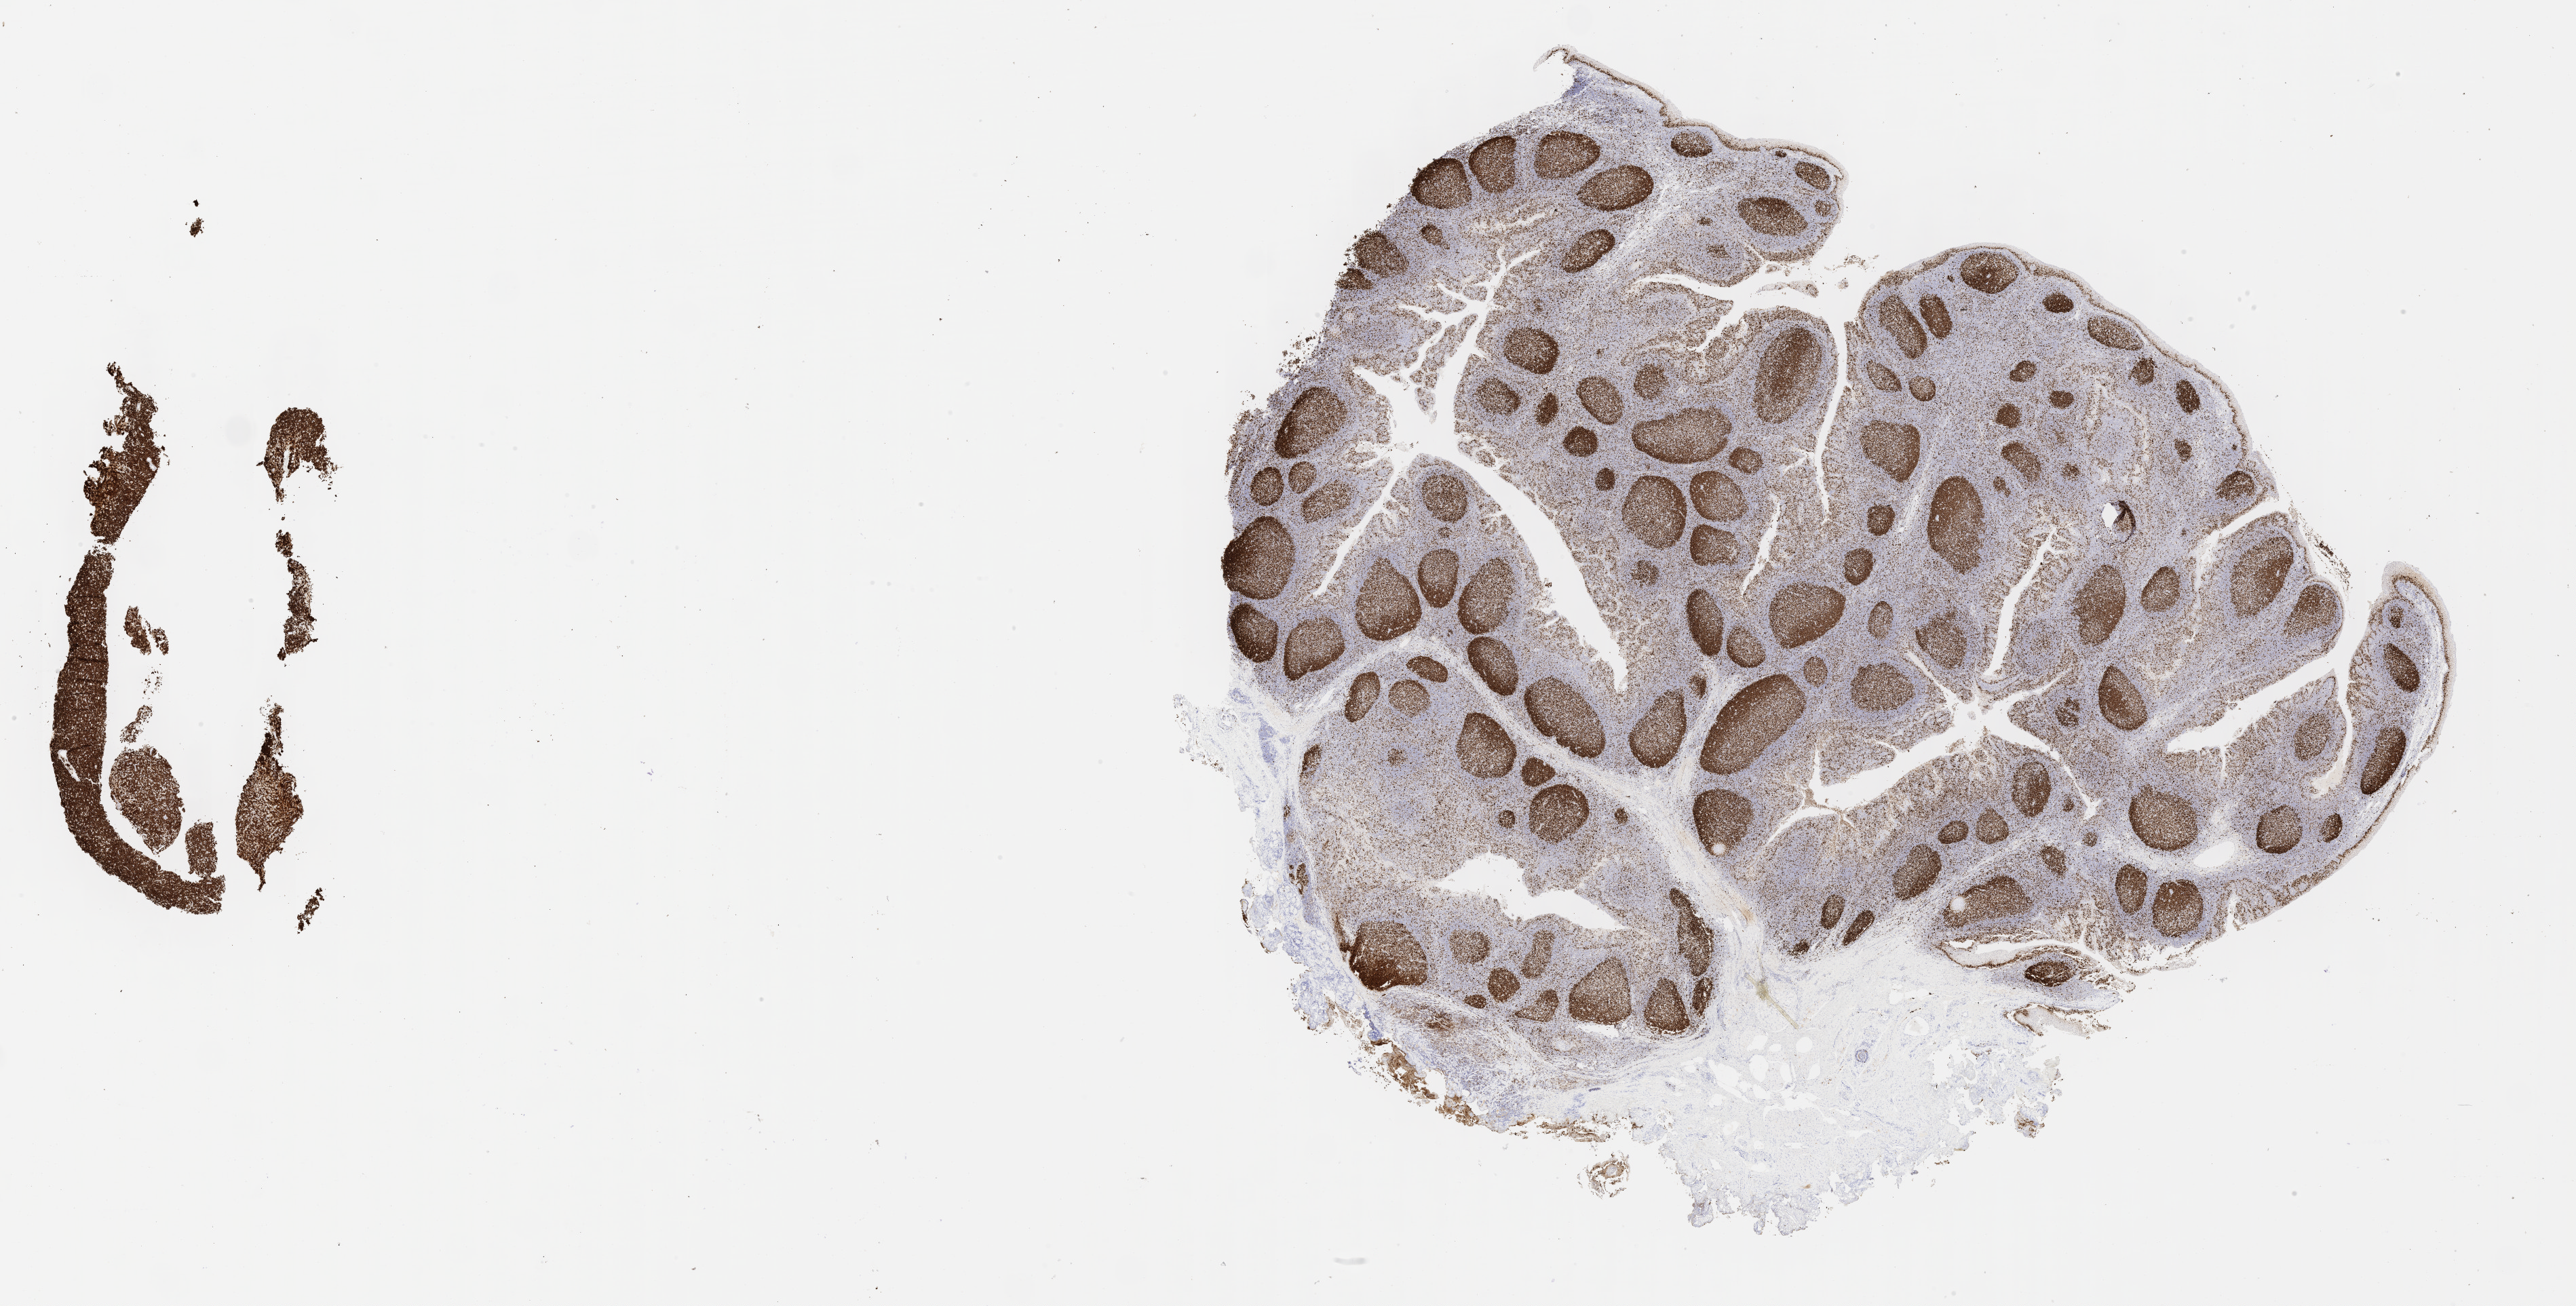
IHC for Ki-67, whole-slide image, shown as a low-resolution overview of the whole scanned area (about 30.7 x 15.6 mm). Specimen: tumor tissue. Patient: female, age 10 years.
Histologic diagnosis: Burkitt lymphoma, NOS.